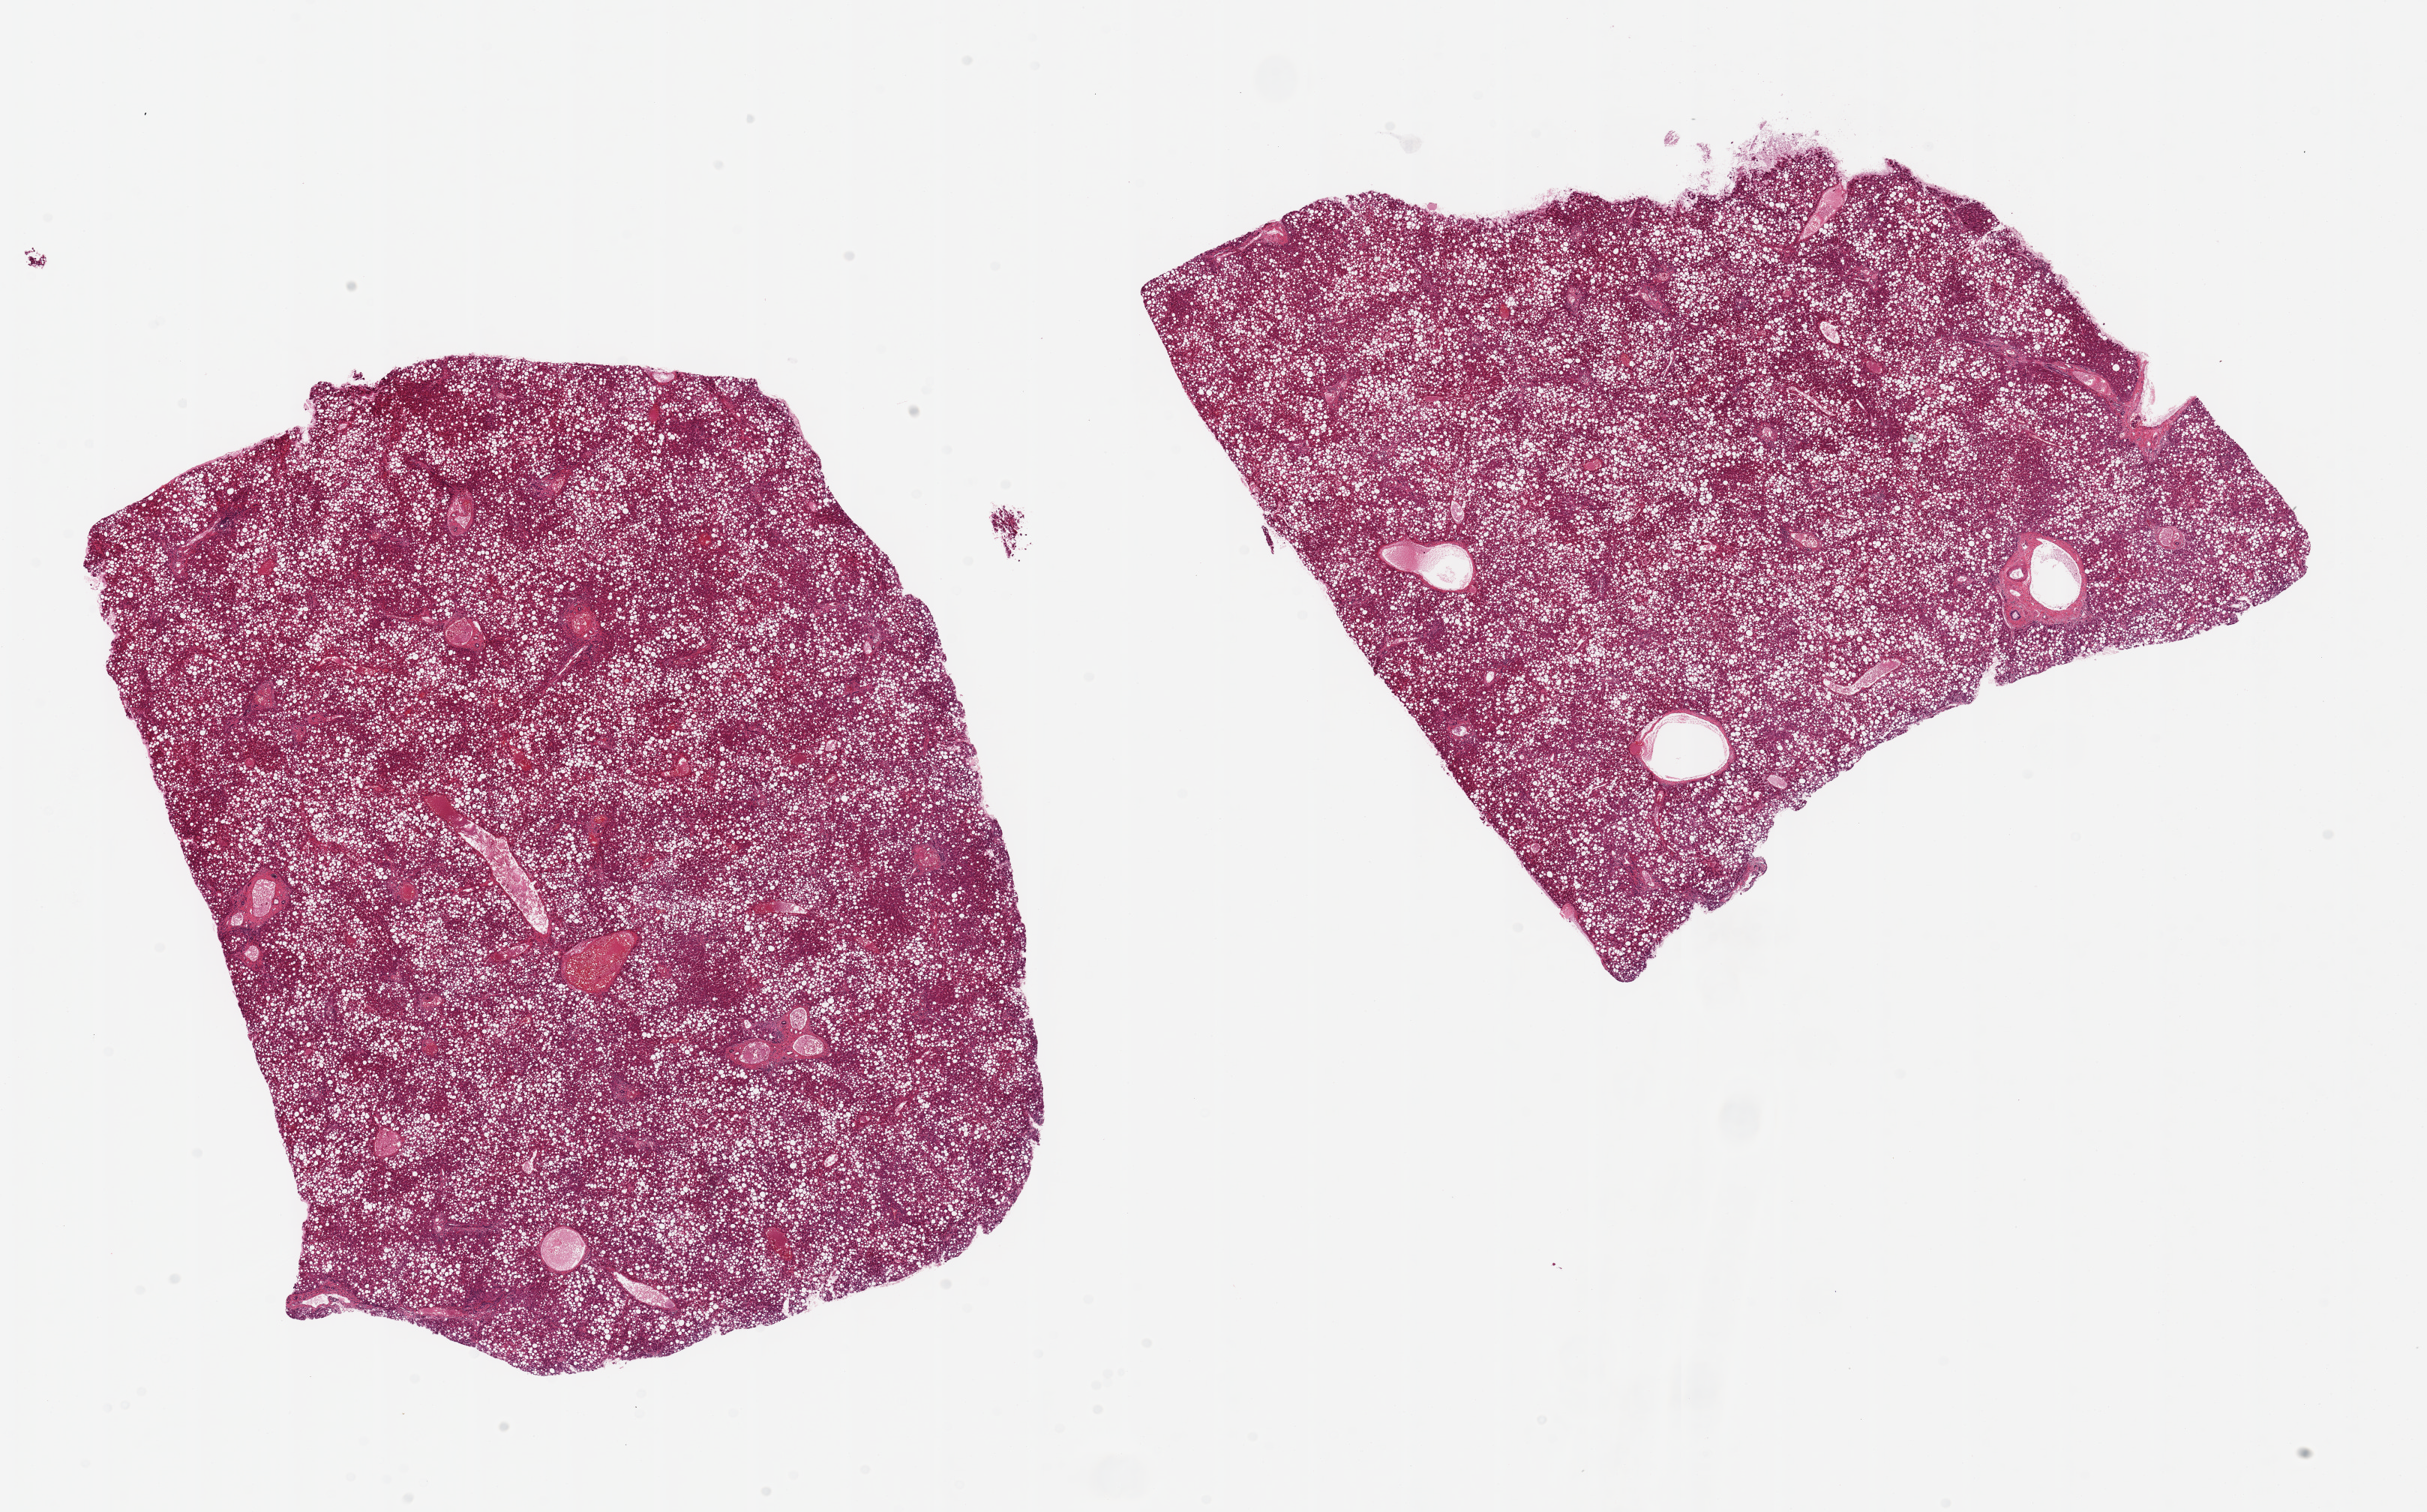
Hematoxylin and eosin (H&E) whole-slide image, brightfield, low-resolution overview of the scanned area, about 25.6 x 15.9 mm (from a 20x scan). PAXgene-fixed paraffin-embedded (PFPE) section. Section of liver (target tissue). Donor tissue sample. Donor sex: male.
• review note (as recorded): 2 pieces, ~9x9mm. Diffuse macrovesicular steatosis involves 90+ % of specimens, which are well - preserved